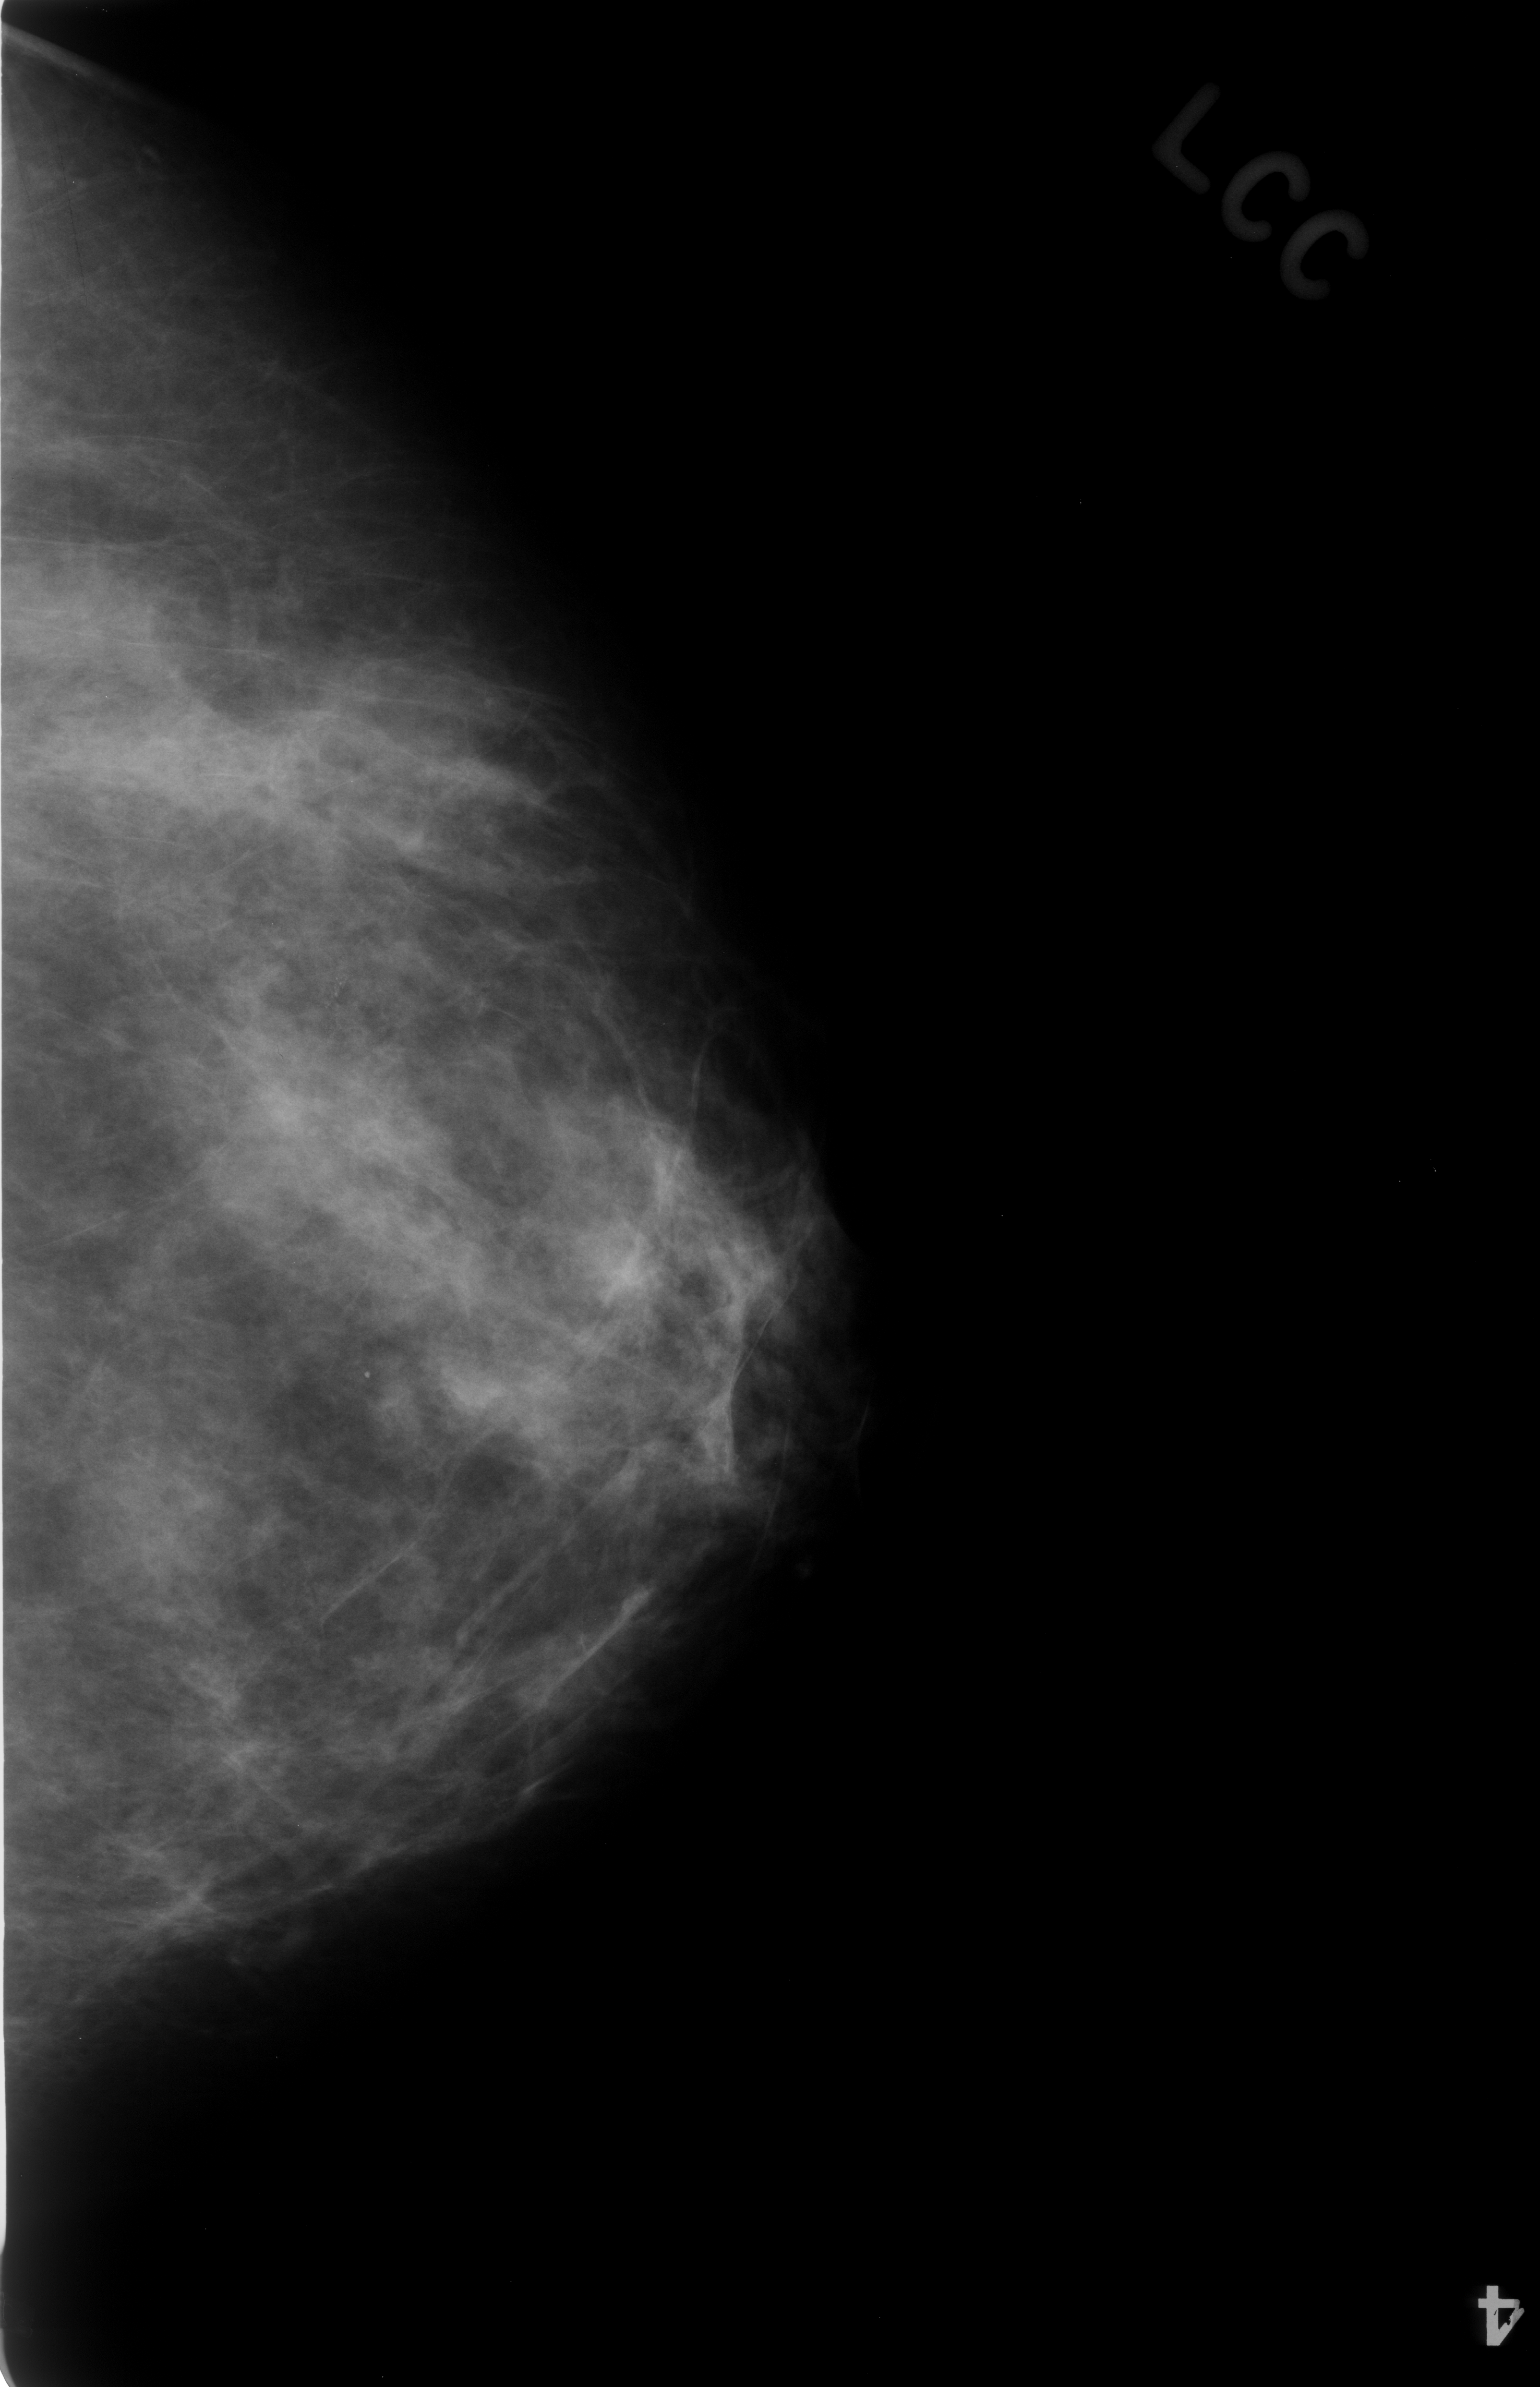
Scanned film-screen mammogram; left breast; CC view; BI-RADS breast density category 2 (scale 1–4); 1540 × 2387 image matrix.
Marked abnormalities (boxes around the expert regions of interest):
- calcifications, morphology amorphous, distribution clustered; BI-RADS assessment category 3; subtlety rating 2 on a 1 (subtle) to 5 (obvious) scale; pathology (as recorded): benign: bounding box <229,909,410,1069> (left, top, right, bottom; pixels)